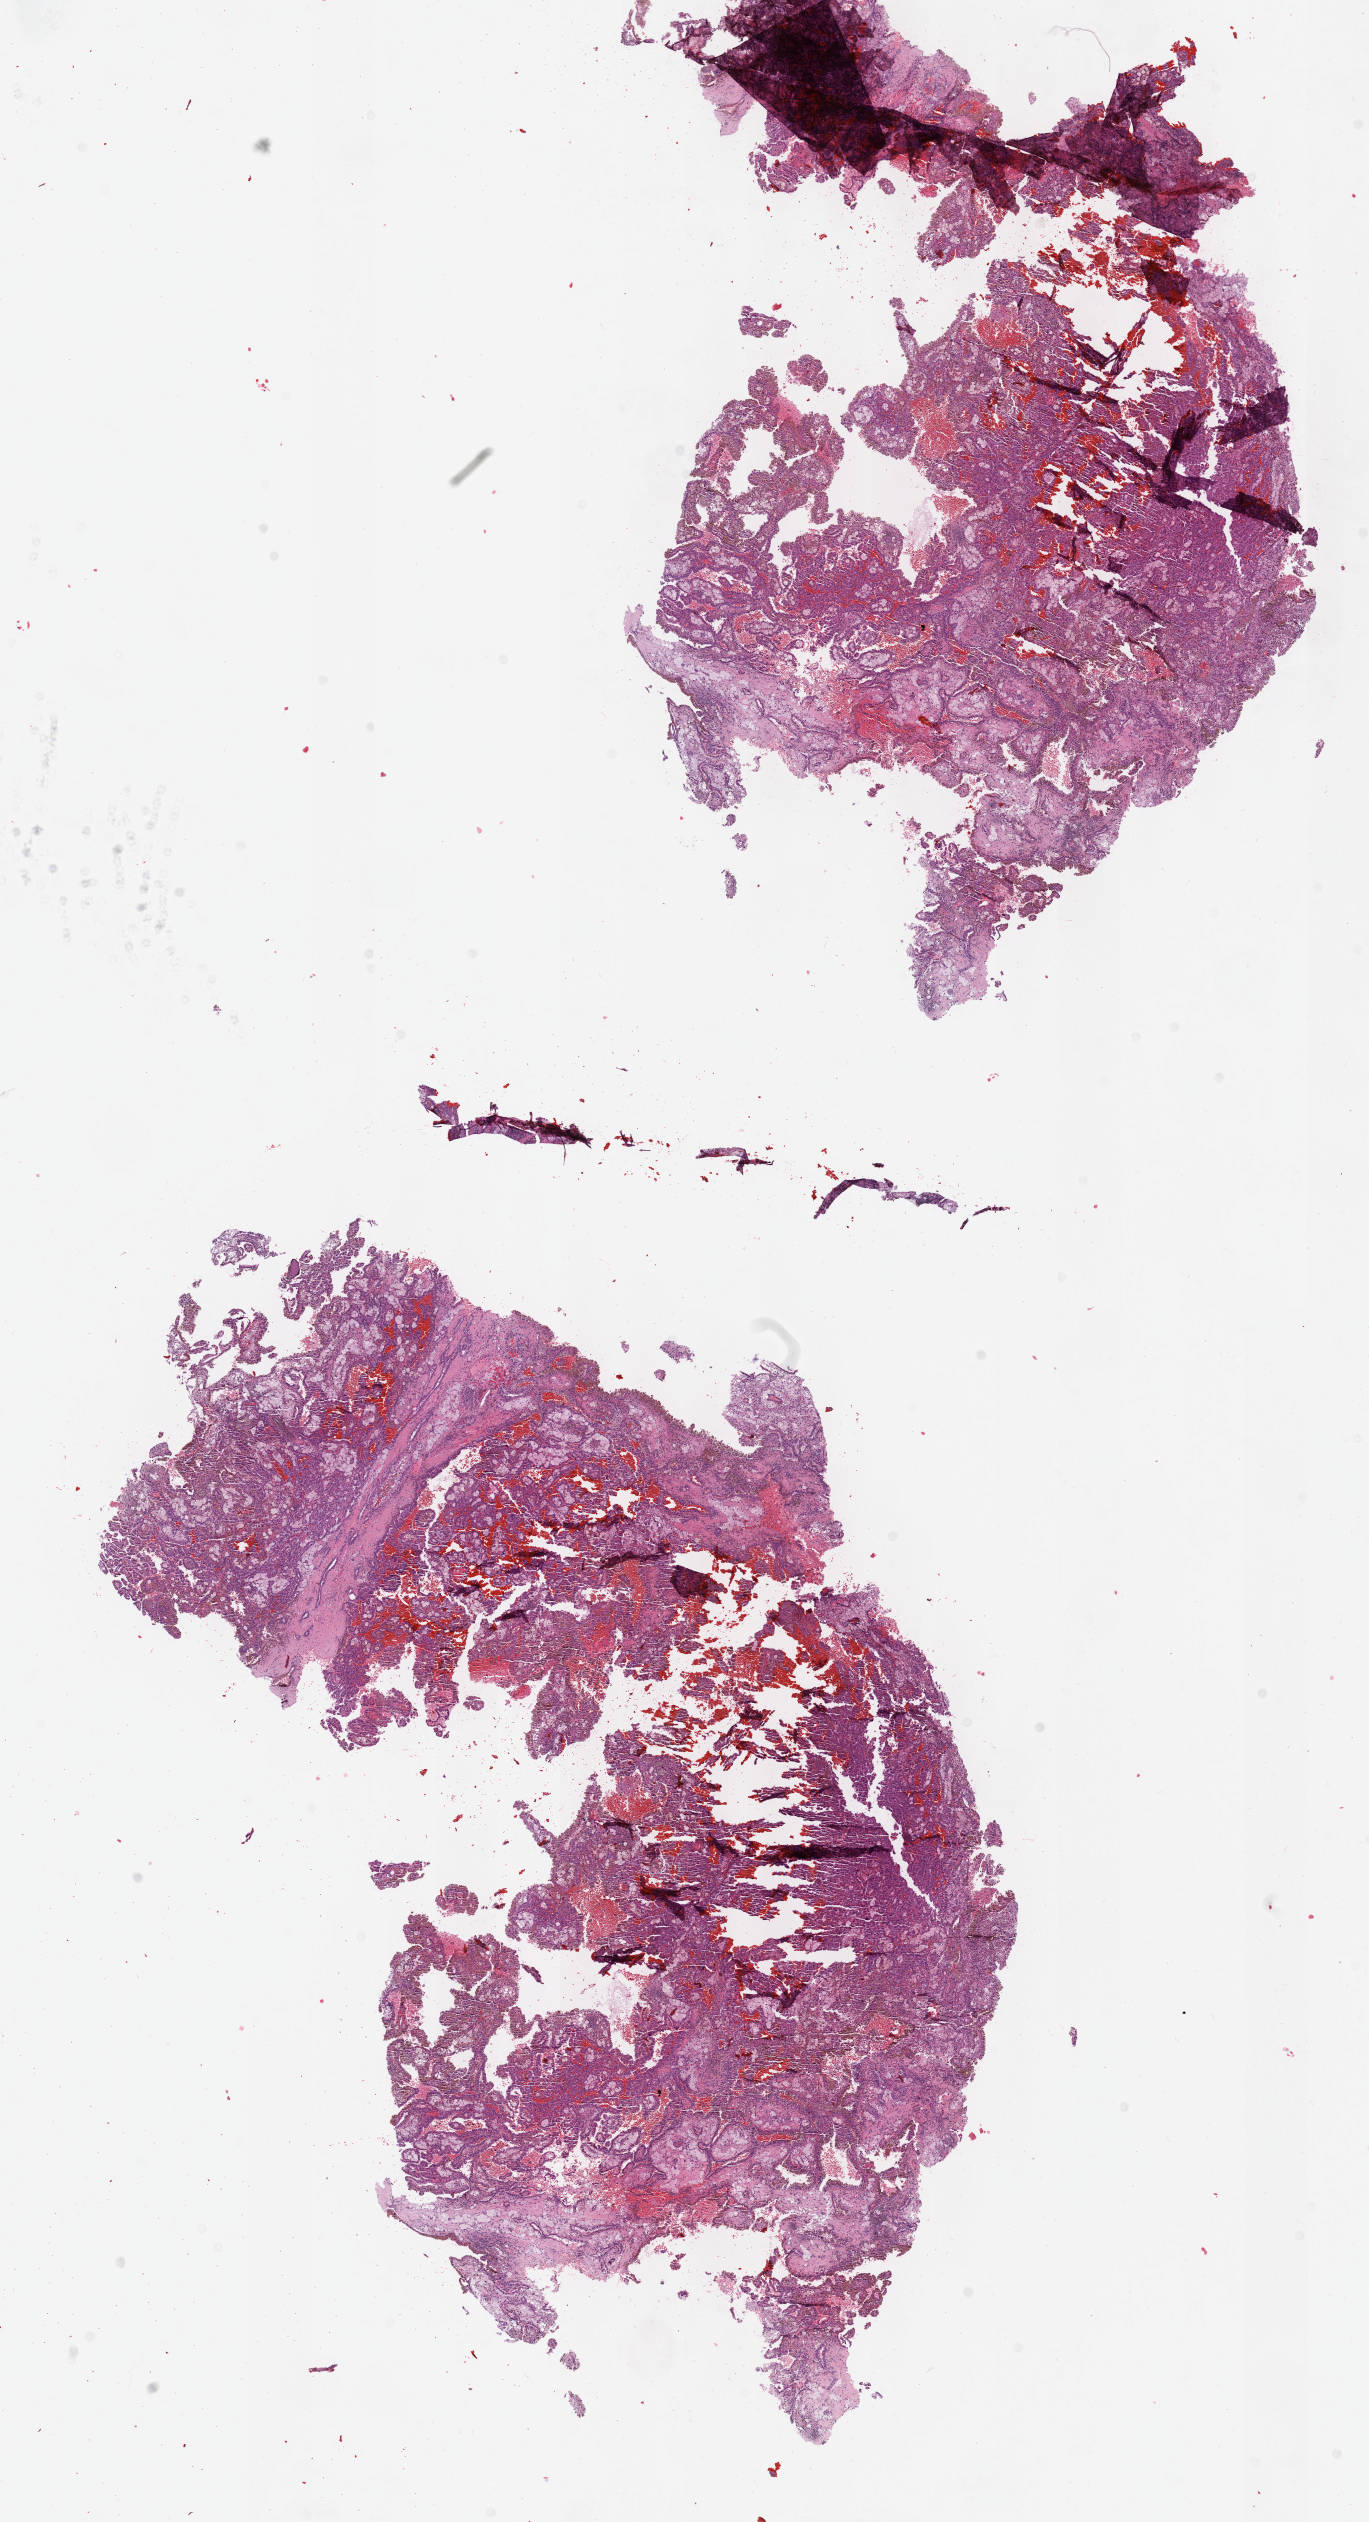
Digitized H&E tissue section (whole slide), shown as a low-resolution overview of the whole scanned area (about 11.1 x 20.4 mm, acquisition: 40x scan), formalin-fixed paraffin-embedded (FFPE) diagnostic section, kidney, primary tumour sample. Male, age 69 years at initial diagnosis.
• AJCC pathologic stage: I (7th edition)
• diagnosis: Papillary adenocarcinoma, NOS